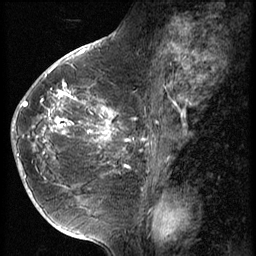
Breast MRI (dynamic contrast-enhanced), one sagittal slice. Position 28 of 56 along the scan axis. 3 images stored at this slice position (order not interpretable as contrast timing). 1.5 T. TE 4.2 ms, TR 9 ms. 2.5 mm slice thickness. 256 × 256 image matrix. Patient: female, 49 years. Case-level facts recorded for this patient, not image findings: setting: breast cancer imaged before/during neoadjuvant chemotherapy; receptor status: HER2-positive.
Structures marked on this image (semi-automatic segmentation, software-assisted and operator-edited):
- analysis volume of interest (the breast-tissue region the enhancement analysis was run in; not a lesion): box from (x=13, y=79) to (x=128, y=203) px
- tumour enhancement mask (voxels above the 140 % enhancement threshold inside the analysis volume of interest): (x=13, y=85)–(x=127, y=173)